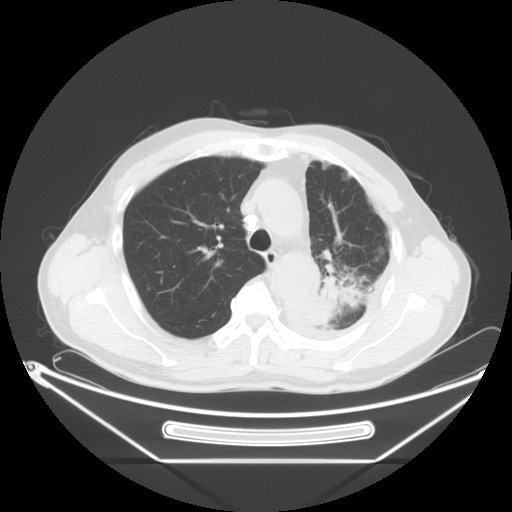
Chest CT, one axial slice; slice 44 of 63 in the series (ordered by position); reconstruction kernel STANDARD; 120 kVp; lung window (W 1500 / L -600 HU); 5 mm slice thickness; 512 × 512 image matrix. Patient: male, 60 years. Case-level facts recorded for this patient, not image findings: clinical TNM (as recorded): T4 N1 M1.
Annotated regions visible in this slice (bounding box drawn by a radiologist):
- lung tumour (recorded histology: adenocarcinoma): bounding box [x1, y1, x2, y2] px = [307, 263, 369, 334]